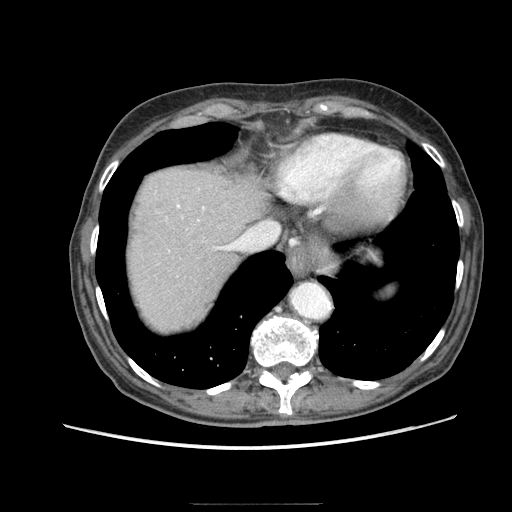
Contrast-enhanced abdominal CT (liver protocol), one axial slice. Slice 72 of 83 in the series (ordered by position). Soft-tissue window (W 400 / L 40 HU). 2.5 mm slice thickness. 512 × 512 image matrix, field of view 360 × 360 mm. From the clinical record (not read from this slice): diagnosis: hepatocellular carcinoma (patient treated with transarterial chemoembolisation; whether this scan precedes or follows treatment is not stated here); TNM stage (as recorded): Stage-I; Child-Pugh class: A; tumour differentiation: moderately differentiated; tumour nodularity: uninodular.
Structures marked on this image (semi-automatic segmentation, software-assisted and operator-edited):
- liver parenchyma outside the tumour (the mass and vessels are separate outlines, so this box may not span the whole liver): bounding box [x1, y1, x2, y2] px = [128, 168, 264, 328]
- liver vessels: [177, 205, 233, 250]